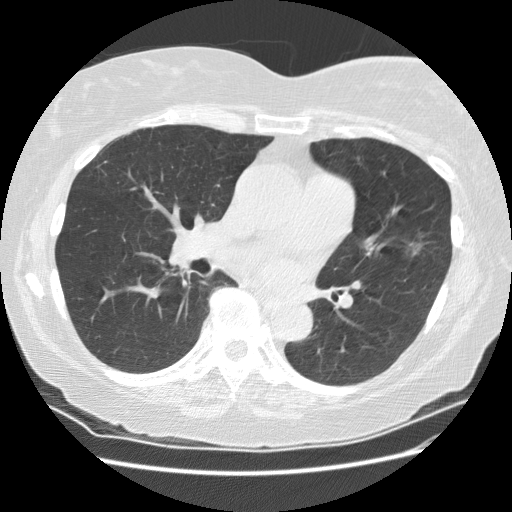
Low-dose screening chest CT, axial slice; second annual screen; lung window (W 1500 / L -600 HU); 2.5 mm slice thickness; standard (soft-tissue) reconstruction kernel (STANDARD); 120 kVp; slice 95 of 180 in the series. Female participant, aged 71 years at enrolment. Former smoker at enrolment.
Lesion marked by an expert reader, bounding box [x1, y1, x2, y2] px = [391, 224, 441, 262]. The exam's reader record, not a measurement of the box and not confirmed to be the same lesion: non-calcified nodule or mass ≥4 mm, lingula, 13 × 13 mm, poorly defined margins, ground glass attenuation, pre-existing on the prior screen: yes; interval growth: yes. Official screen result: positive, change unspecified: nodule(s) >= 4 mm or enlarging nodule(s), mass(es), or other non-specific abnormalities suspicious for lung cancer. Later outcome: lung cancer diagnosed 26 days after this screen — adenocarcinoma, NOS, left upper lobe, well differentiated (G1), stage IA (AJCC 6th edition), 11 mm at pathology.